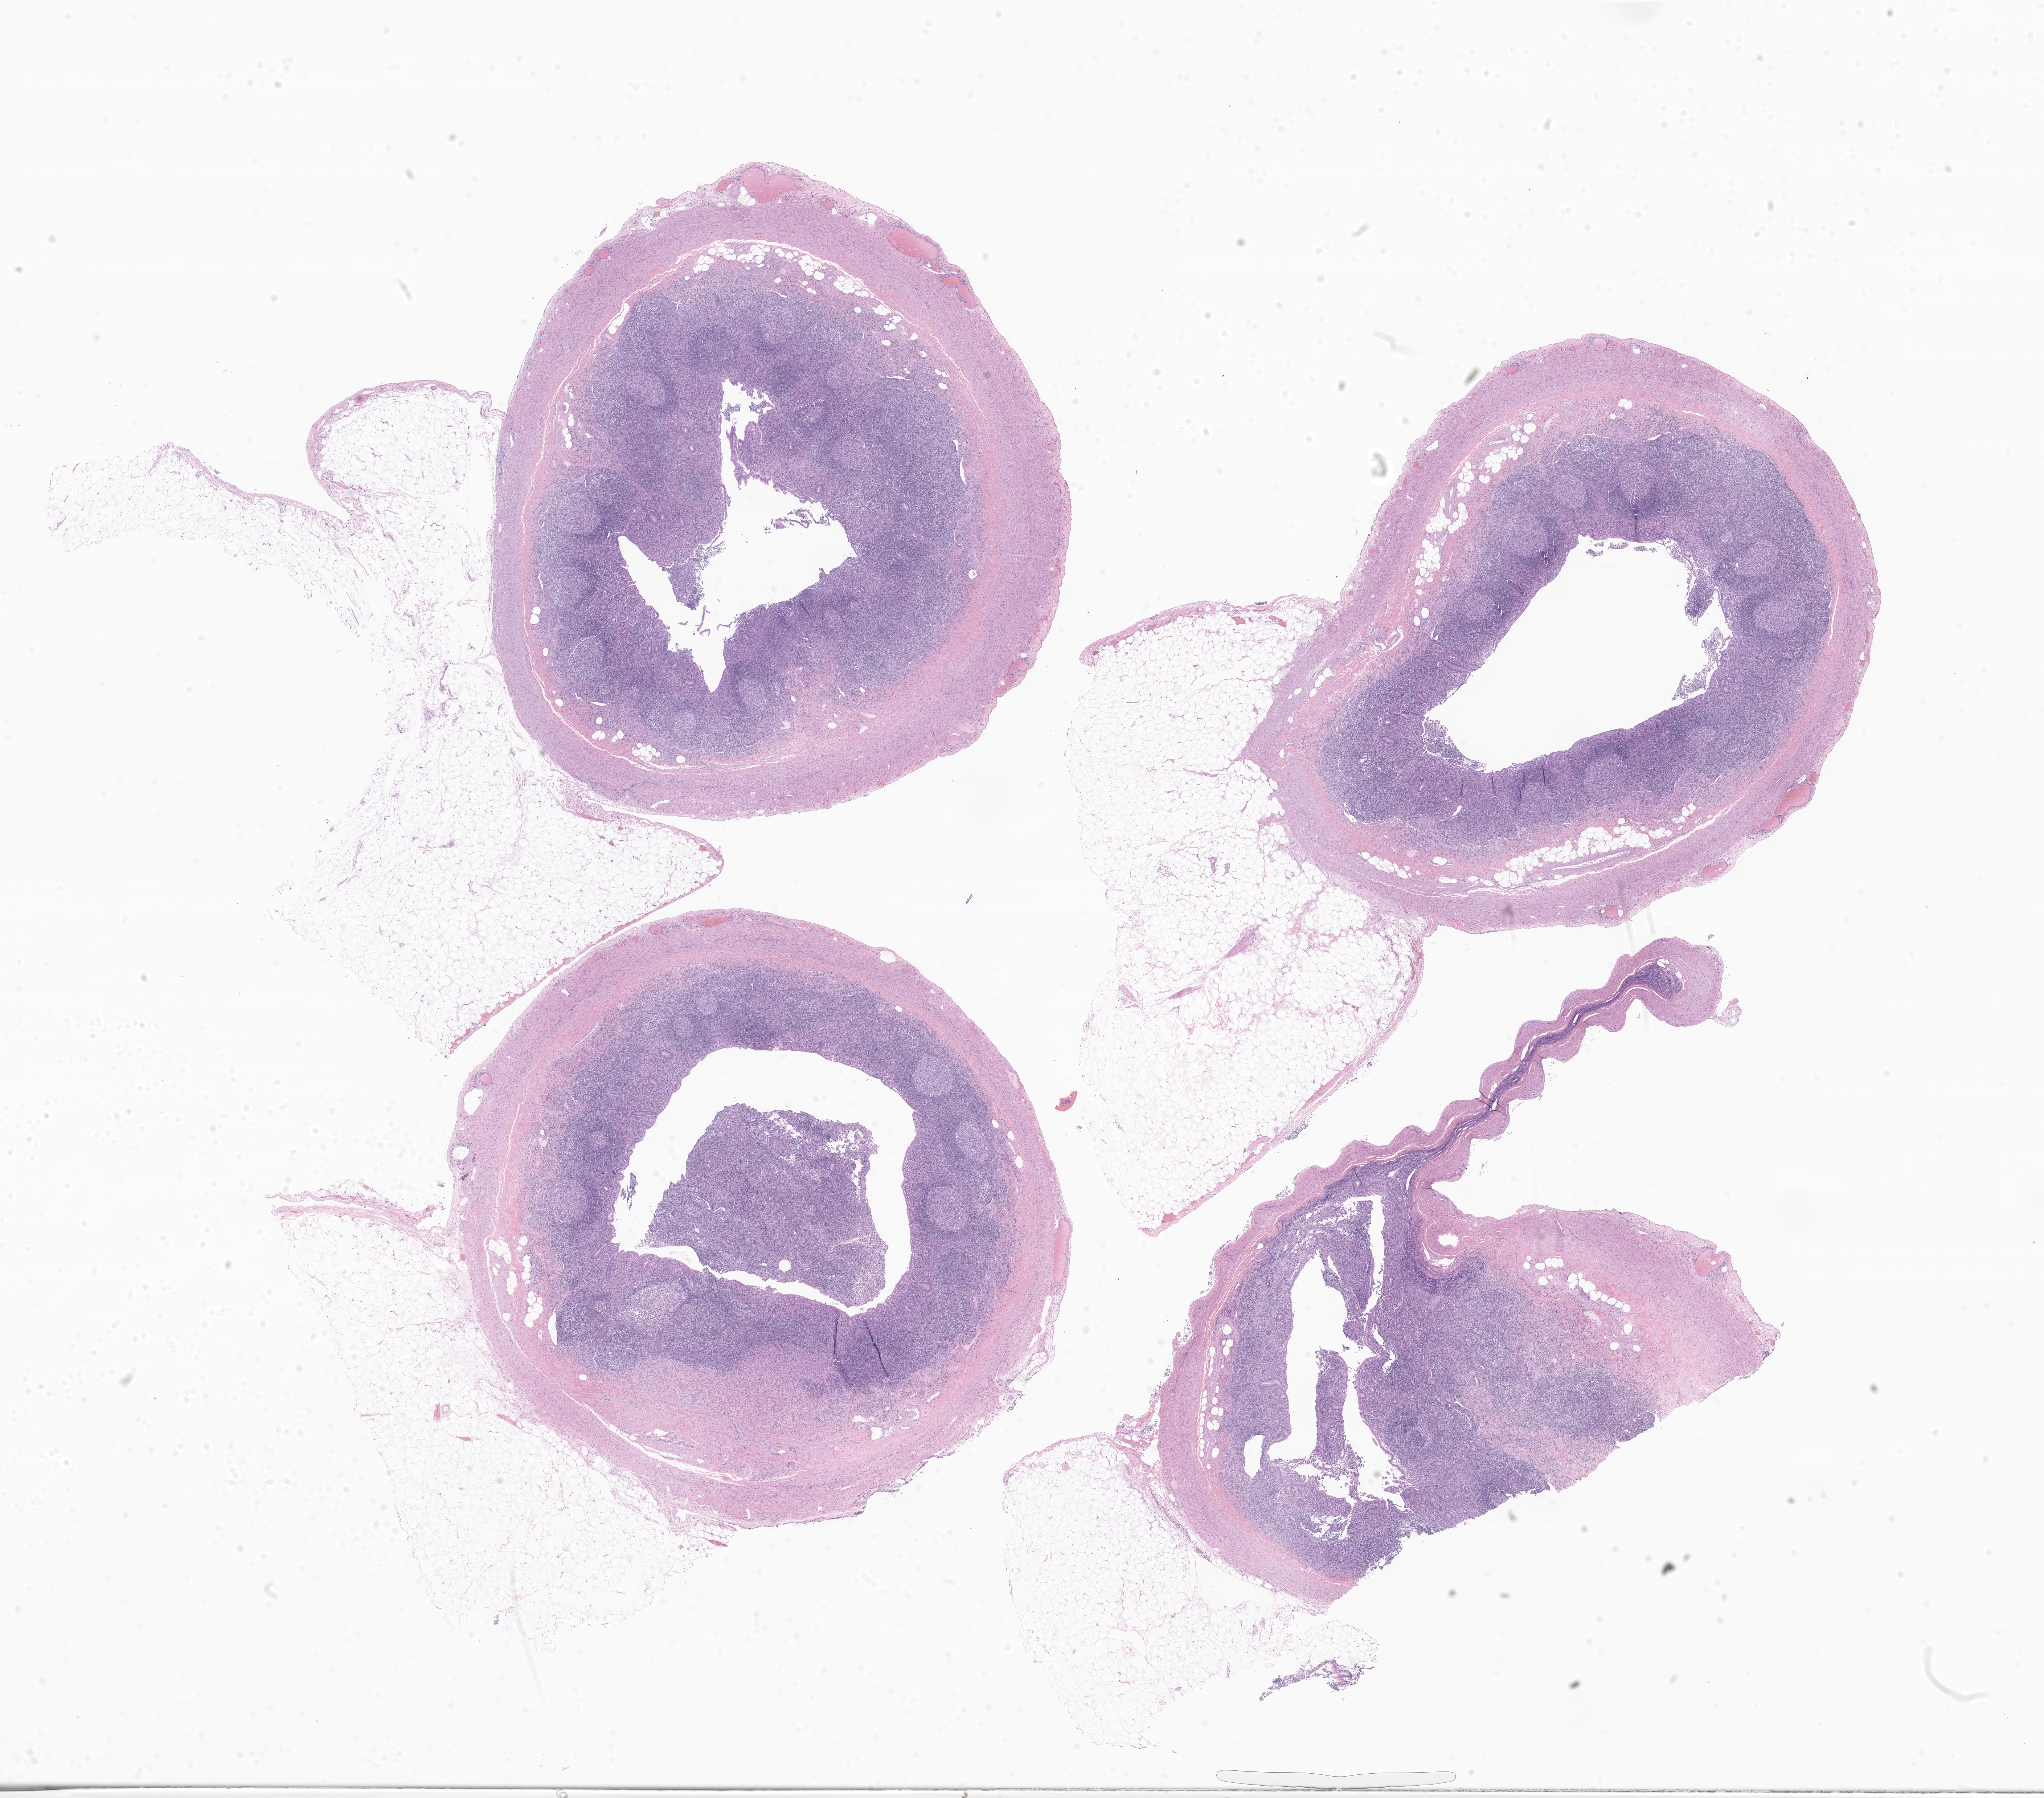
H&E whole-slide image of tumor tissue from the appendix — whole scanned area (about 23.7 x 20.9 mm) shown as a low-resolution overview. Patient female; age 172 months (14 years 4 months).
Specimen: FFPE section.